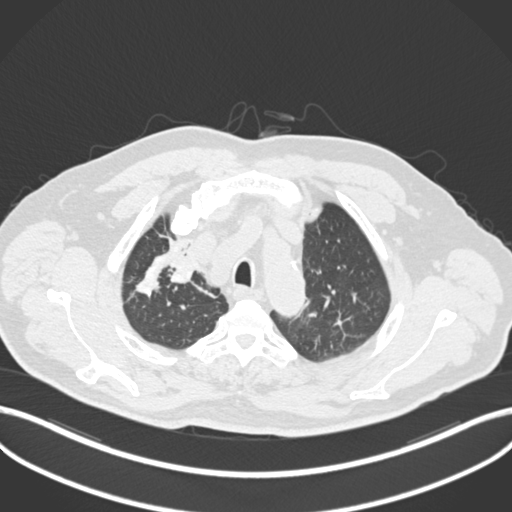
Chest CT, one axial slice. Position 166 of 255 along the scan axis. 120 kVp. Lung window (W 1500 / L -600 HU). 512 × 512 image matrix. Male patient, age 60 years. From the clinical record (not read from this slice): clinical TNM (as recorded): T1b N1 M0.
Annotated regions visible in this slice (bounding box drawn by a radiologist):
- lung tumour (recorded histology: squamous cell carcinoma): bounding box (x1, y1, x2, y2) in pixels: (160, 243, 202, 293)